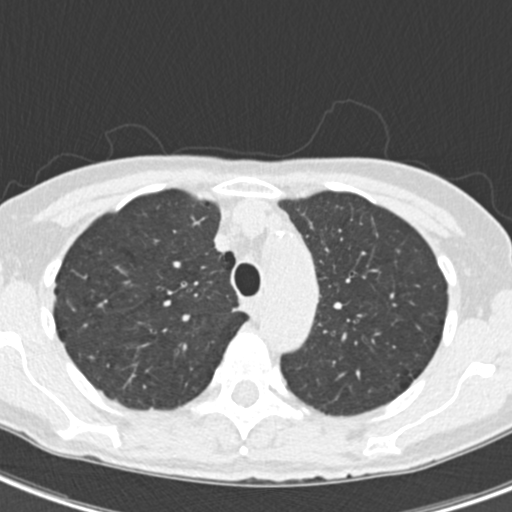
Chest CT (low-dose screening protocol), one axial image; second screening round (one year after baseline); lung window (W 1500 / L -600 HU); 120 kVp; 512 × 512 image matrix, field of view 286 × 286 mm. Female, age 68 years at enrolment. Current smoker at enrolment.
Expert-annotated lung lesion, bounding box [x1, y1, x2, y2] px = [223, 299, 253, 326]. No non-calcified nodule or mass ≥4 mm was recorded by the screening reader at this exam. Later outcome: lung cancer diagnosed 436 days after this screen (after the third annual screen) — squamous cell carcinoma, NOS, right upper lobe, mediastinum, poorly differentiated (G3), stage IIIB (AJCC 6th edition), 43 mm at pathology.